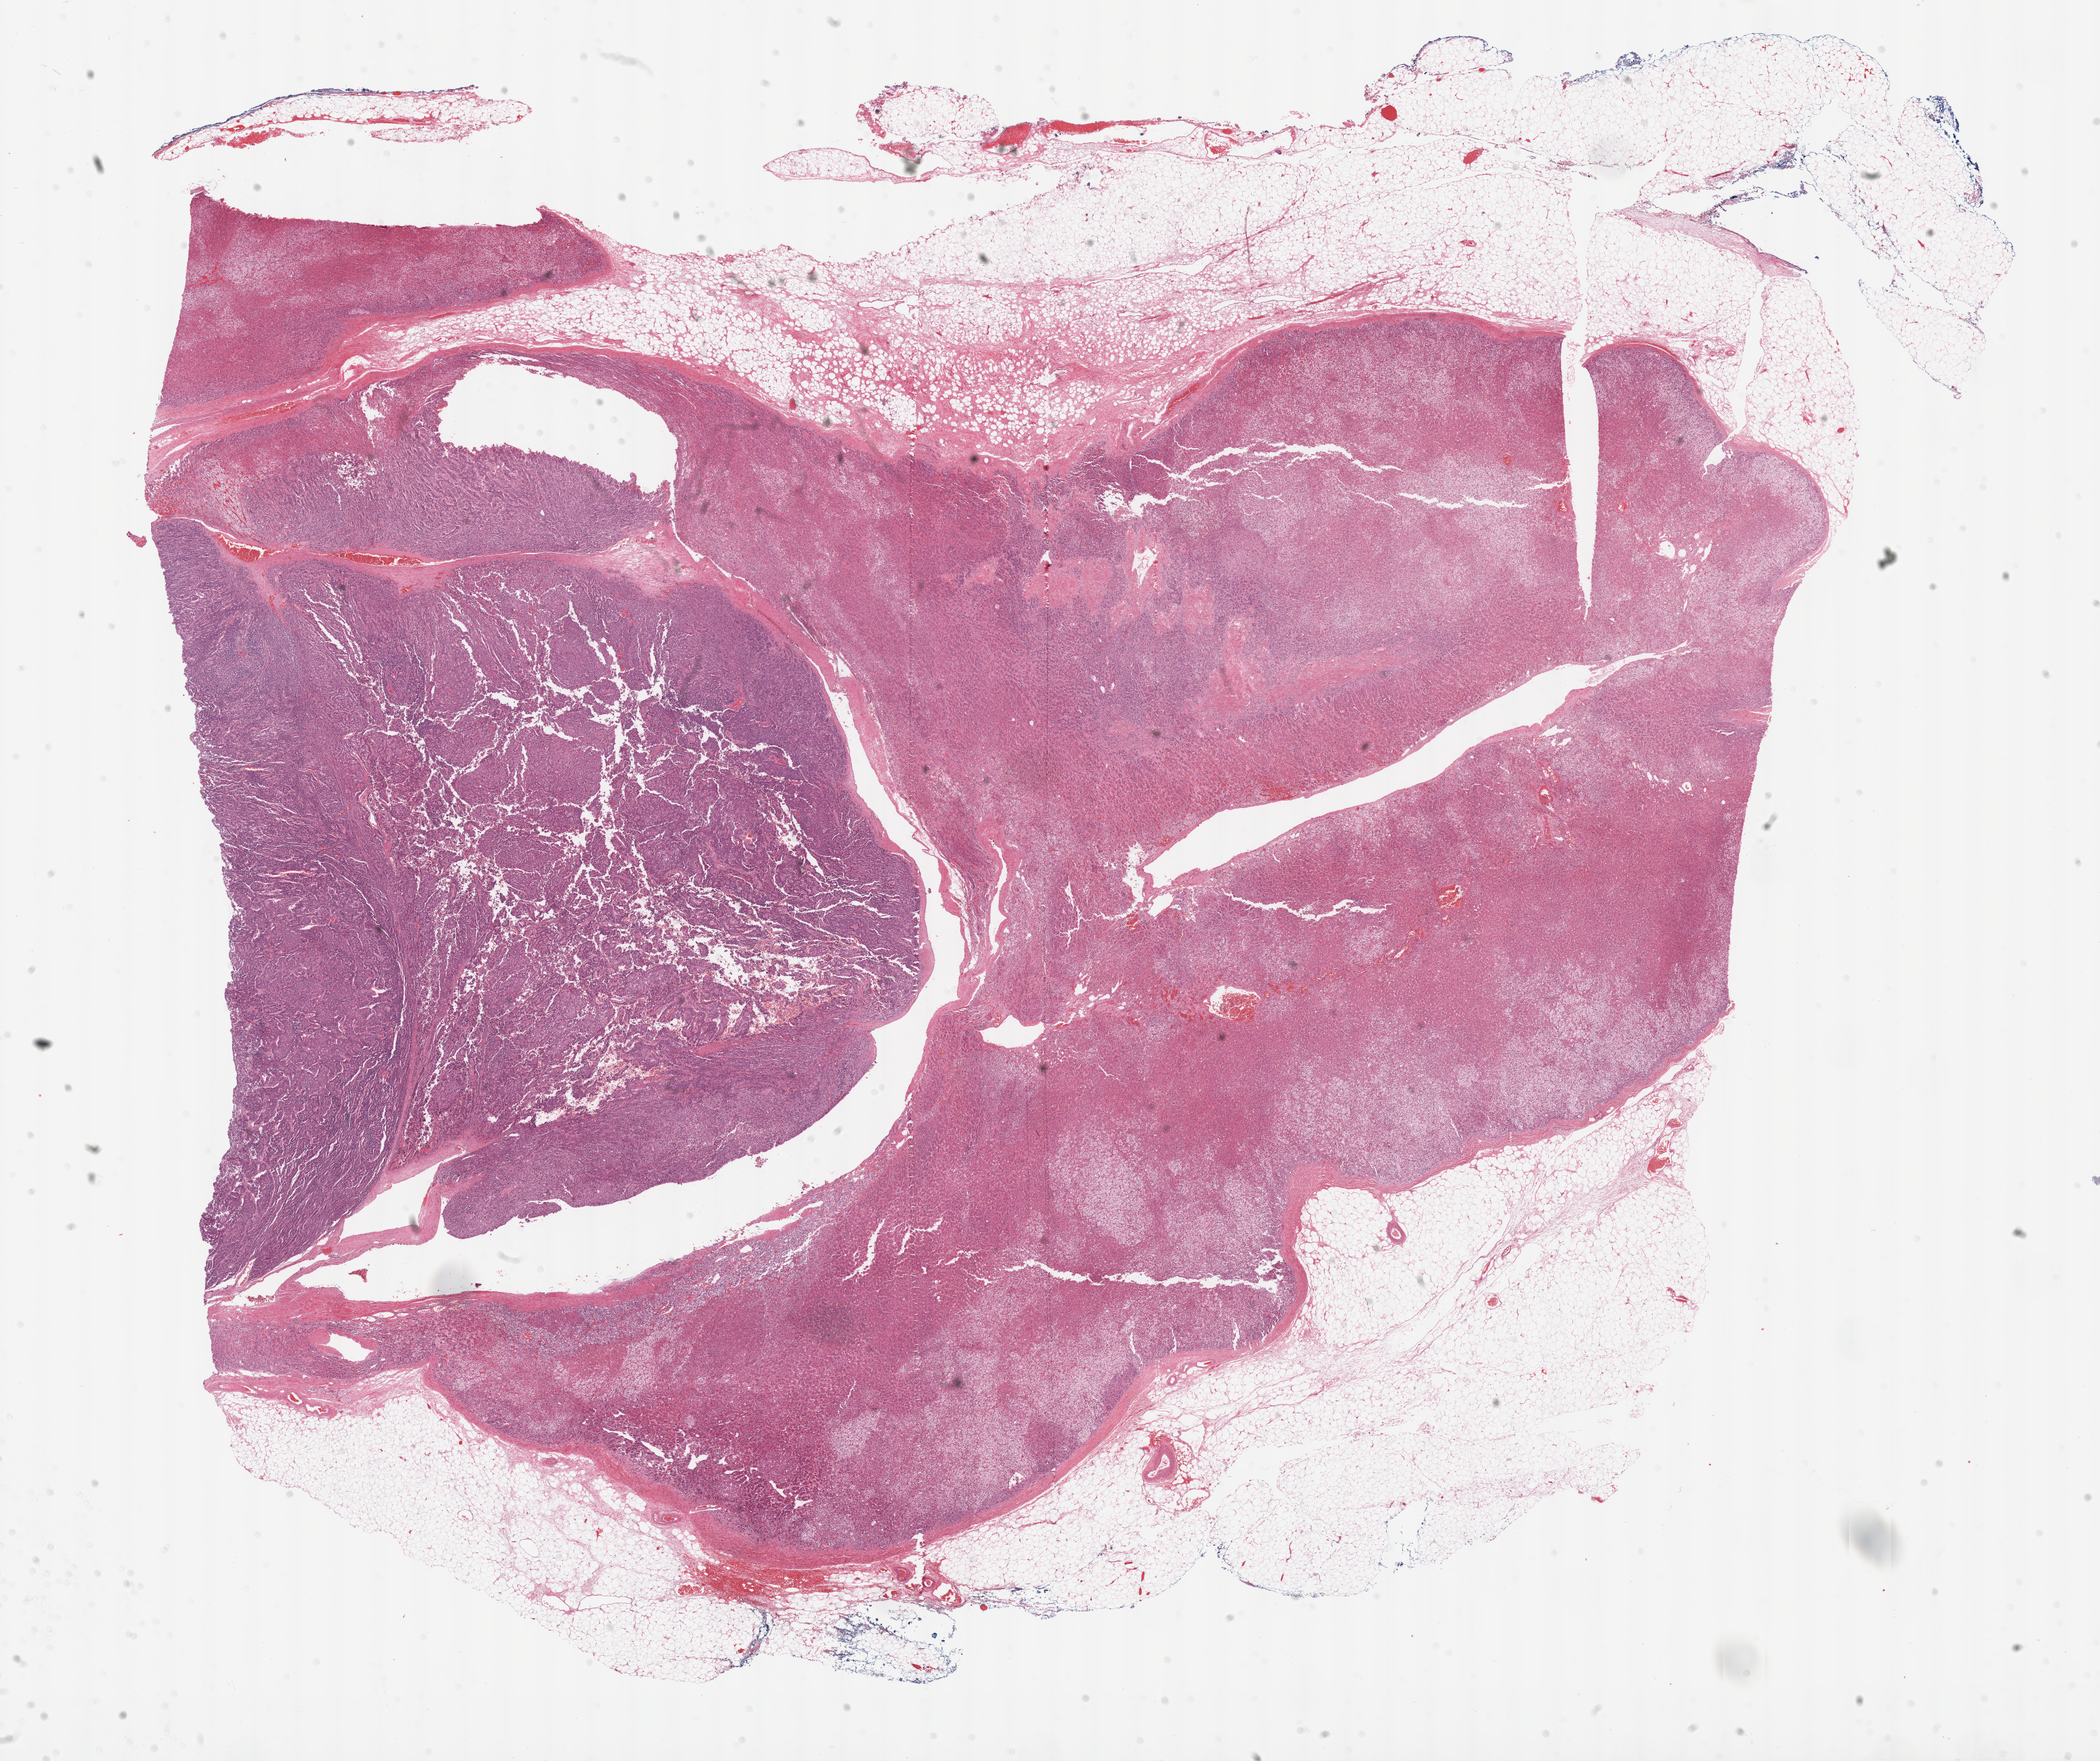
Digitized H&E tissue section (whole slide), shown as a low-resolution overview of the whole scanned area (about 25.2 x 21.1 mm, slide scanned at 40x), FFPE section, adrenal cortex, primary tumour sample. Male, age 58 years at initial diagnosis.
- histologic diagnosis: Adrenal cortical carcinoma (cortex of adrenal gland)